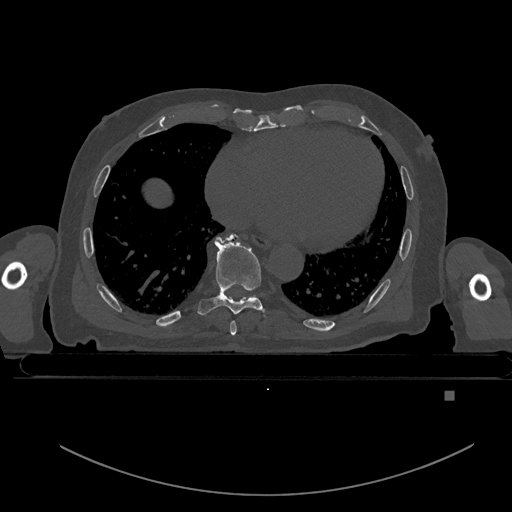
CT including the spine, one axial slice. Position 200 of 969 along the scan axis. Bone window (W 1800 / L 400 HU). 0.5 mm slice thickness. 512 × 512 image matrix, field of view 456 × 456 mm. Patient: male, 82 years. From the clinical record (not read from this slice): primary cancer: prostate; vertebrae with lytic lesions (as recorded): T11, T9, T8, T2.
Structures marked on this image (semi-automatically segmented with operator editing):
- T7 vertebra: box from (x=230, y=321) to (x=236, y=335) px
- T8 vertebra: (x=197, y=235)–(x=271, y=319)
- T9 vertebra: (x=230, y=235)–(x=234, y=239)